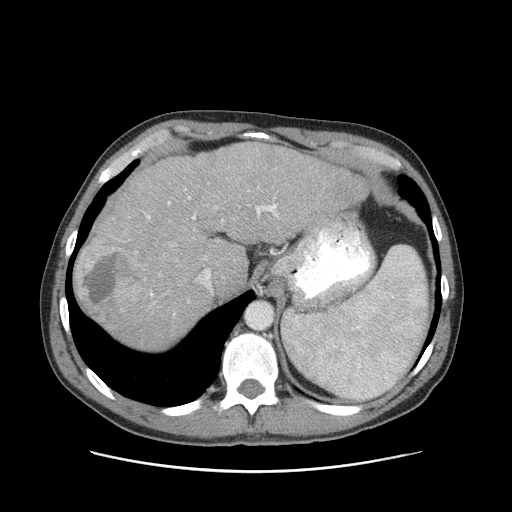
Contrast-enhanced abdominal CT (liver protocol), one axial slice. Slice 74 of 93 in the series (ordered by position). Reconstruction kernel STANDARD. 120 kVp. Soft-tissue window (W 400 / L 40 HU). 2.5 mm slice thickness. 512 × 512 image matrix, field of view 380 × 380 mm. Case-level facts recorded for this patient, not image findings: diagnosis: hepatocellular carcinoma (patient treated with transarterial chemoembolisation; whether this scan precedes or follows treatment is not stated here); TNM stage (as recorded): Stage-II; Child-Pugh class: A; tumour differentiation: moderately differentiated; tumour size: 1 cm.
Annotated regions visible in this slice (semi-automatic segmentation, software-assisted and operator-edited):
- abdominal aorta: bounding box <247,303,271,328> (left, top, right, bottom; pixels)
- liver parenchyma outside the tumour (the mass and vessels are separate outlines, so this box may not span the whole liver): <76,142,368,348>
- mass: <79,246,145,322>
- liver vessels: <147,197,278,296>